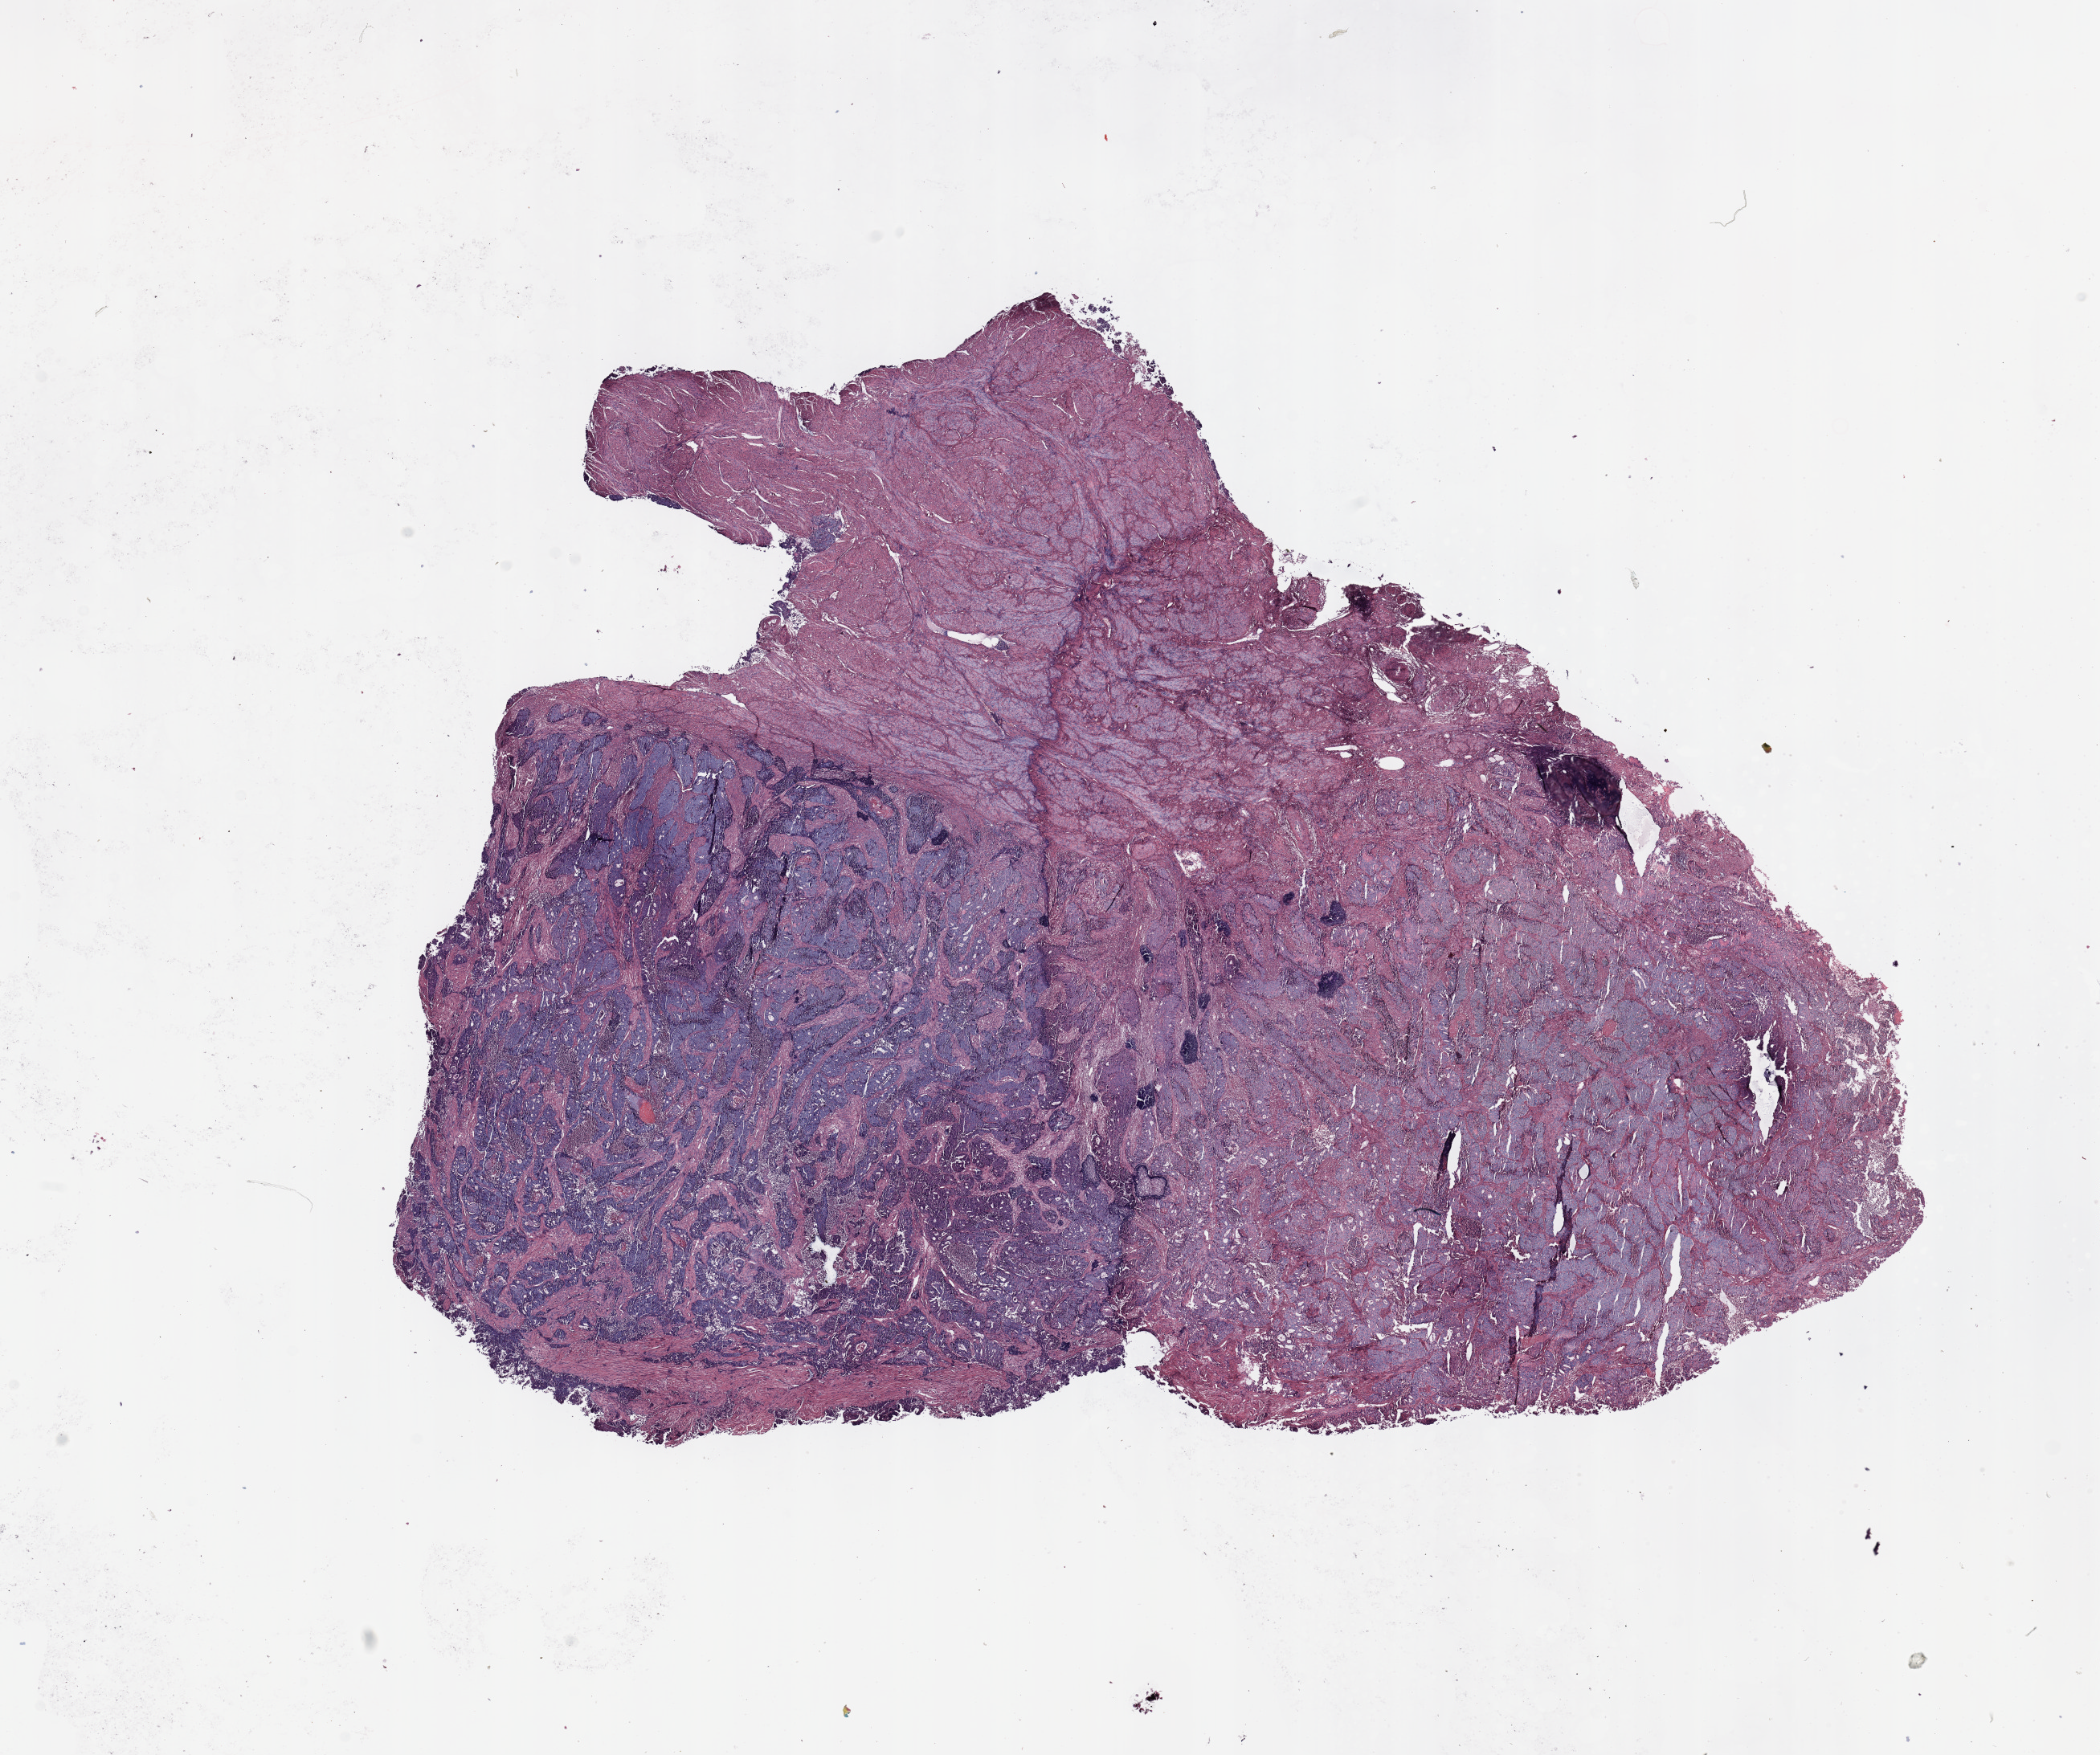
H&E-stained whole-slide image — whole scanned area (about 20.7 x 17.3 mm) shown as a low-resolution overview. Tumour tissue sample, uterus. Female, 59 y/o. Histologic grade: G2 (moderately differentiated).
Diagnosis: Endometrioid adenocarcinoma, NOS. AJCC pathologic stage: II.